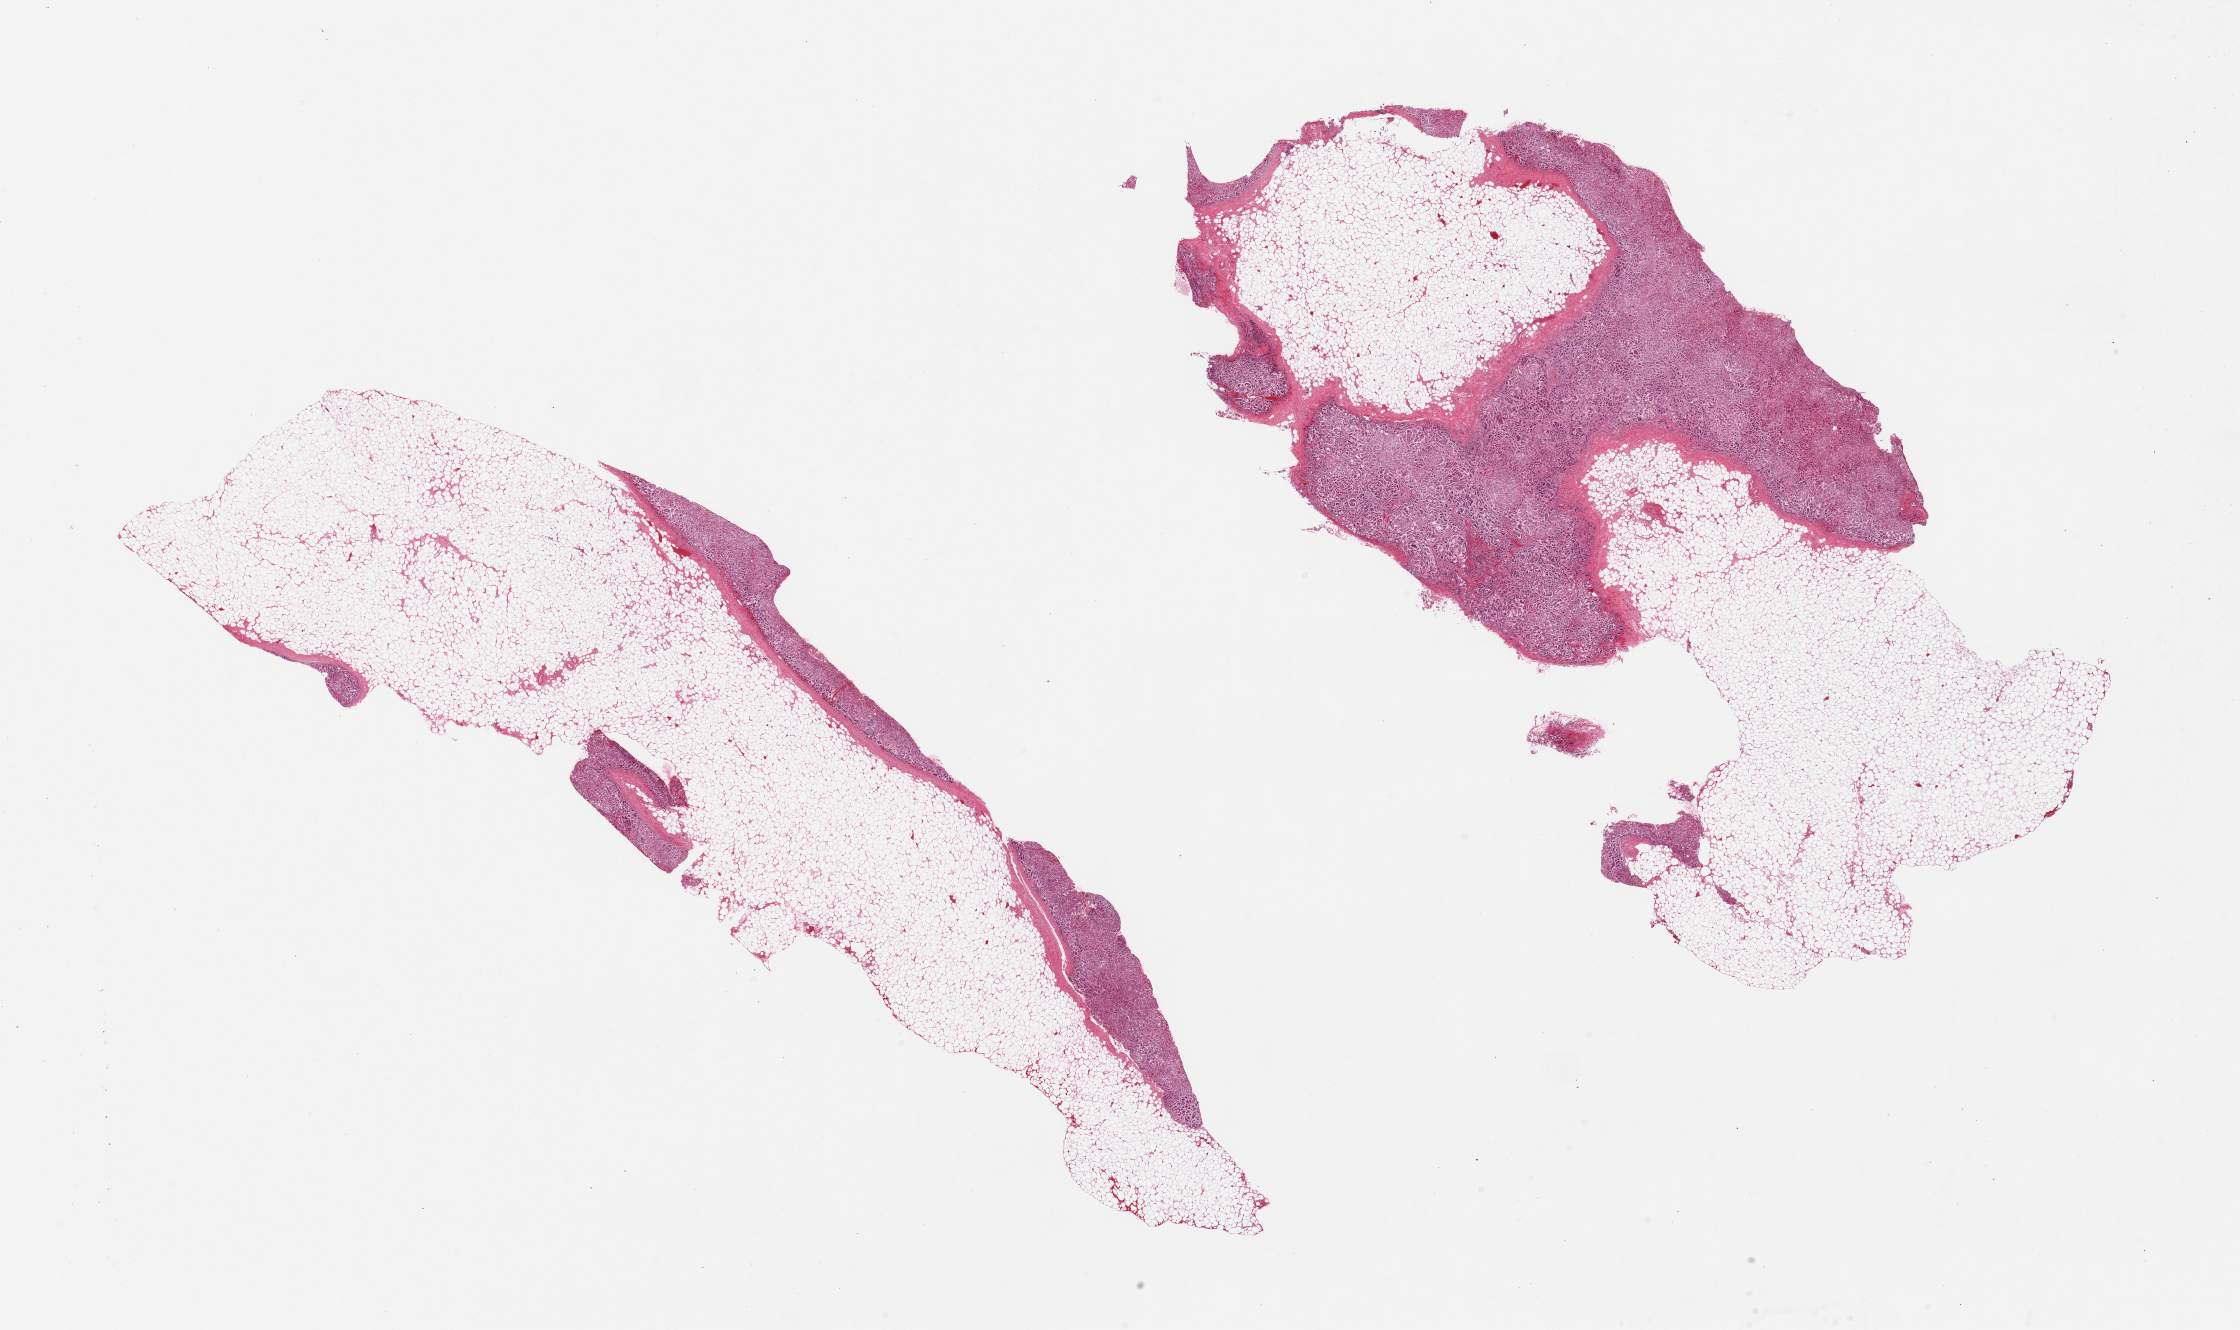
Digitized haematoxylin and eosin-stained section, whole scanned area (about 35.4 x 21.0 mm, slide scanned at 20x) shown as a low-resolution overview. PAXgene-fixed, paraffin-embedded tissue. Target tissue: adrenal gland. Donor tissue sample. Male donor.
Pathologist's review note for this sample: 2 pieces, one is 90% fat, second is 60% fat.